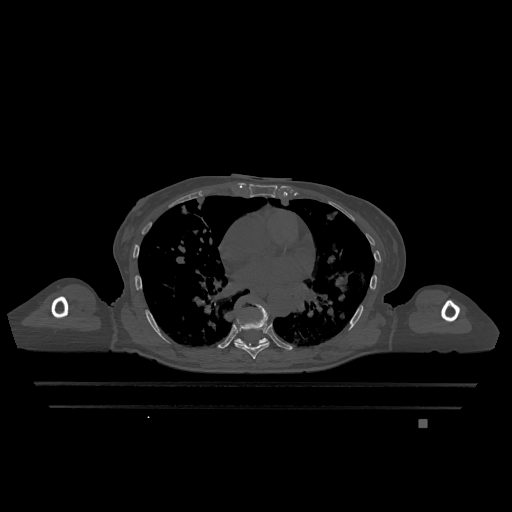
CT including the spine, one axial slice; position 724 of 1317 along the scan axis; bone window (W 1800 / L 400 HU); 0.5 mm slice thickness; 512 × 512 image matrix, field of view 500 × 500 mm. Patient: female, 74 years. From the clinical record (not read from this slice): primary cancer: lung.
Annotated regions visible in this slice (semi-automatically segmented with operator editing):
- T7 vertebra: bounding box (x1, y1, x2, y2) in pixels: (234, 303, 270, 359)
- T9 vertebra: (234, 337, 268, 345)